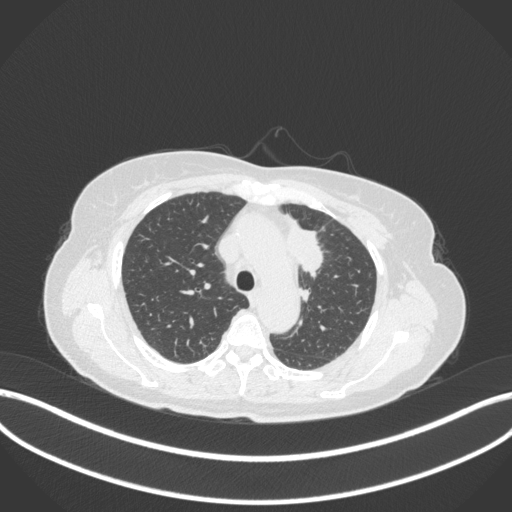
Chest CT, one axial slice. Lung window (W 1500 / L -600 HU). 1 mm slice thickness. 512 × 512 image matrix, field of view 400 × 400 mm. Female patient, age 65 years. Case-level facts recorded for this patient, not image findings: clinical TNM (as recorded): T2a N0 M0; histopathological grade: G2-3.
Outlined on this slice (rectangle marked by the reading radiologist):
- lung tumour (recorded histology: adenocarcinoma): box from (x=285, y=219) to (x=326, y=280) px